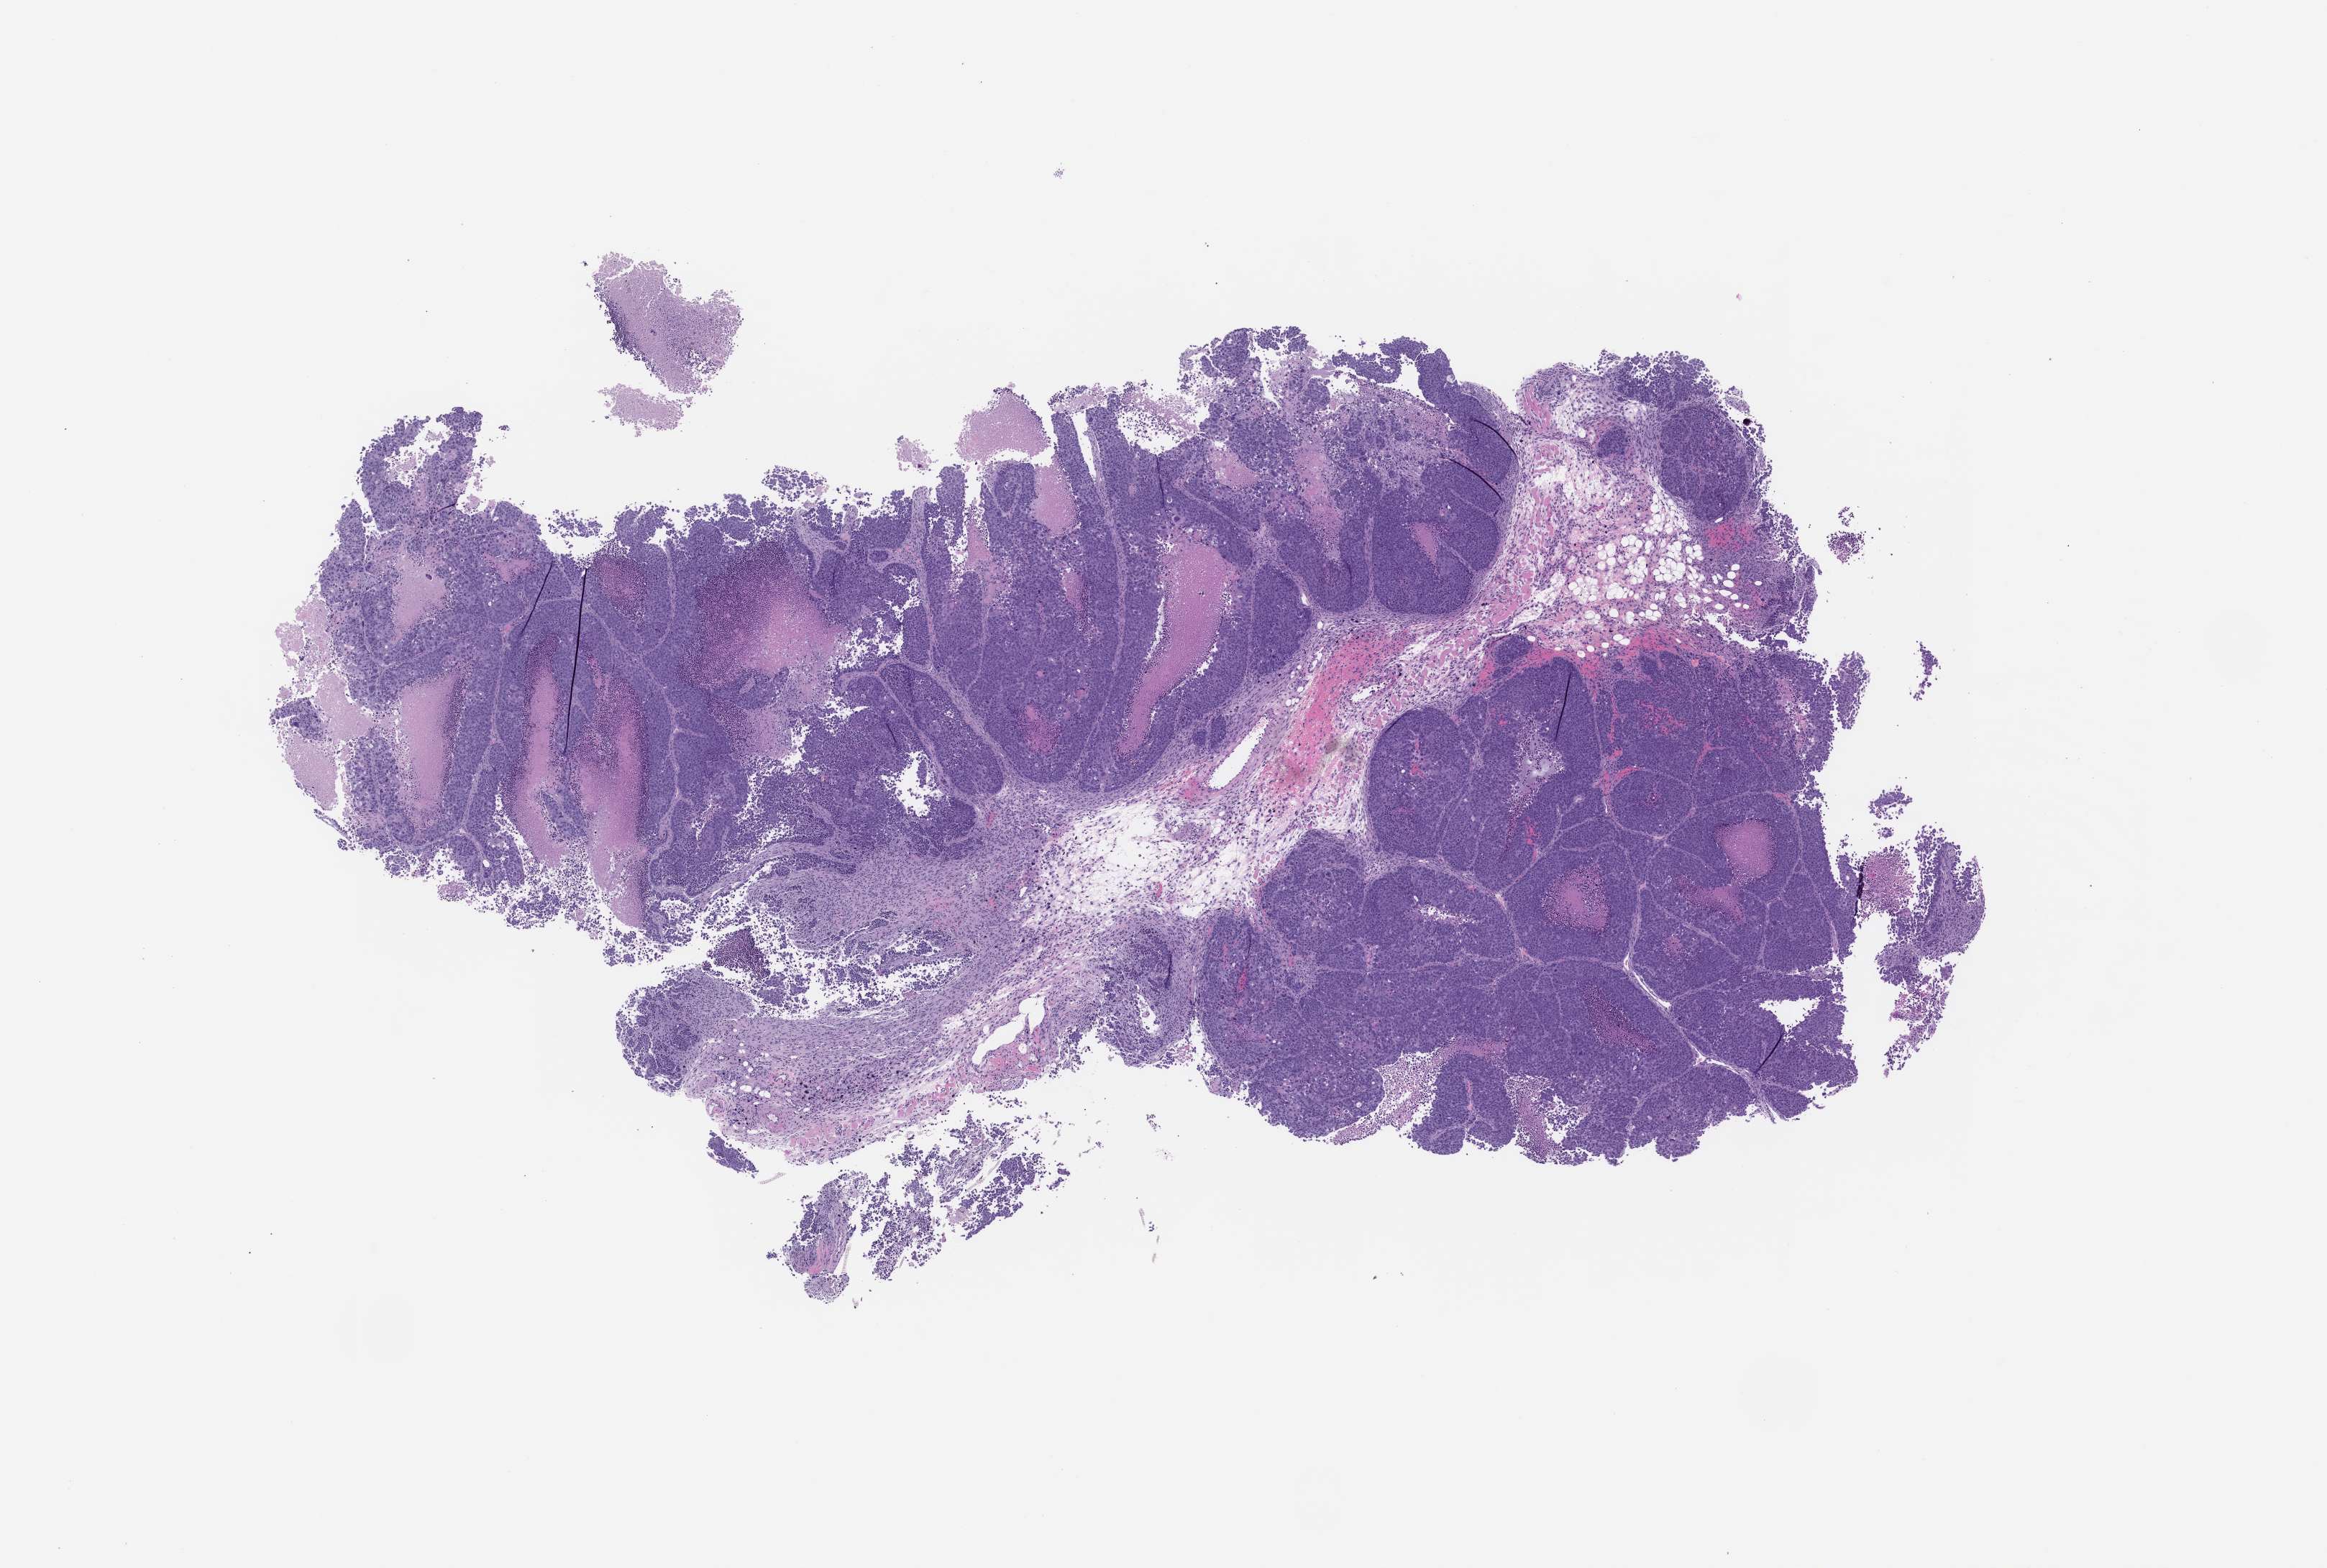
Whole-slide image, H&E: patient-derived xenograft (human tumor grown in a mouse), passage 1, shown as a low-resolution overview of the whole scanned area (about 13.0 x 8.7 mm); FFPE section; originating tumor site category: lung.
Originating patient diagnosis: Lung Squamous Cell Carcinoma.